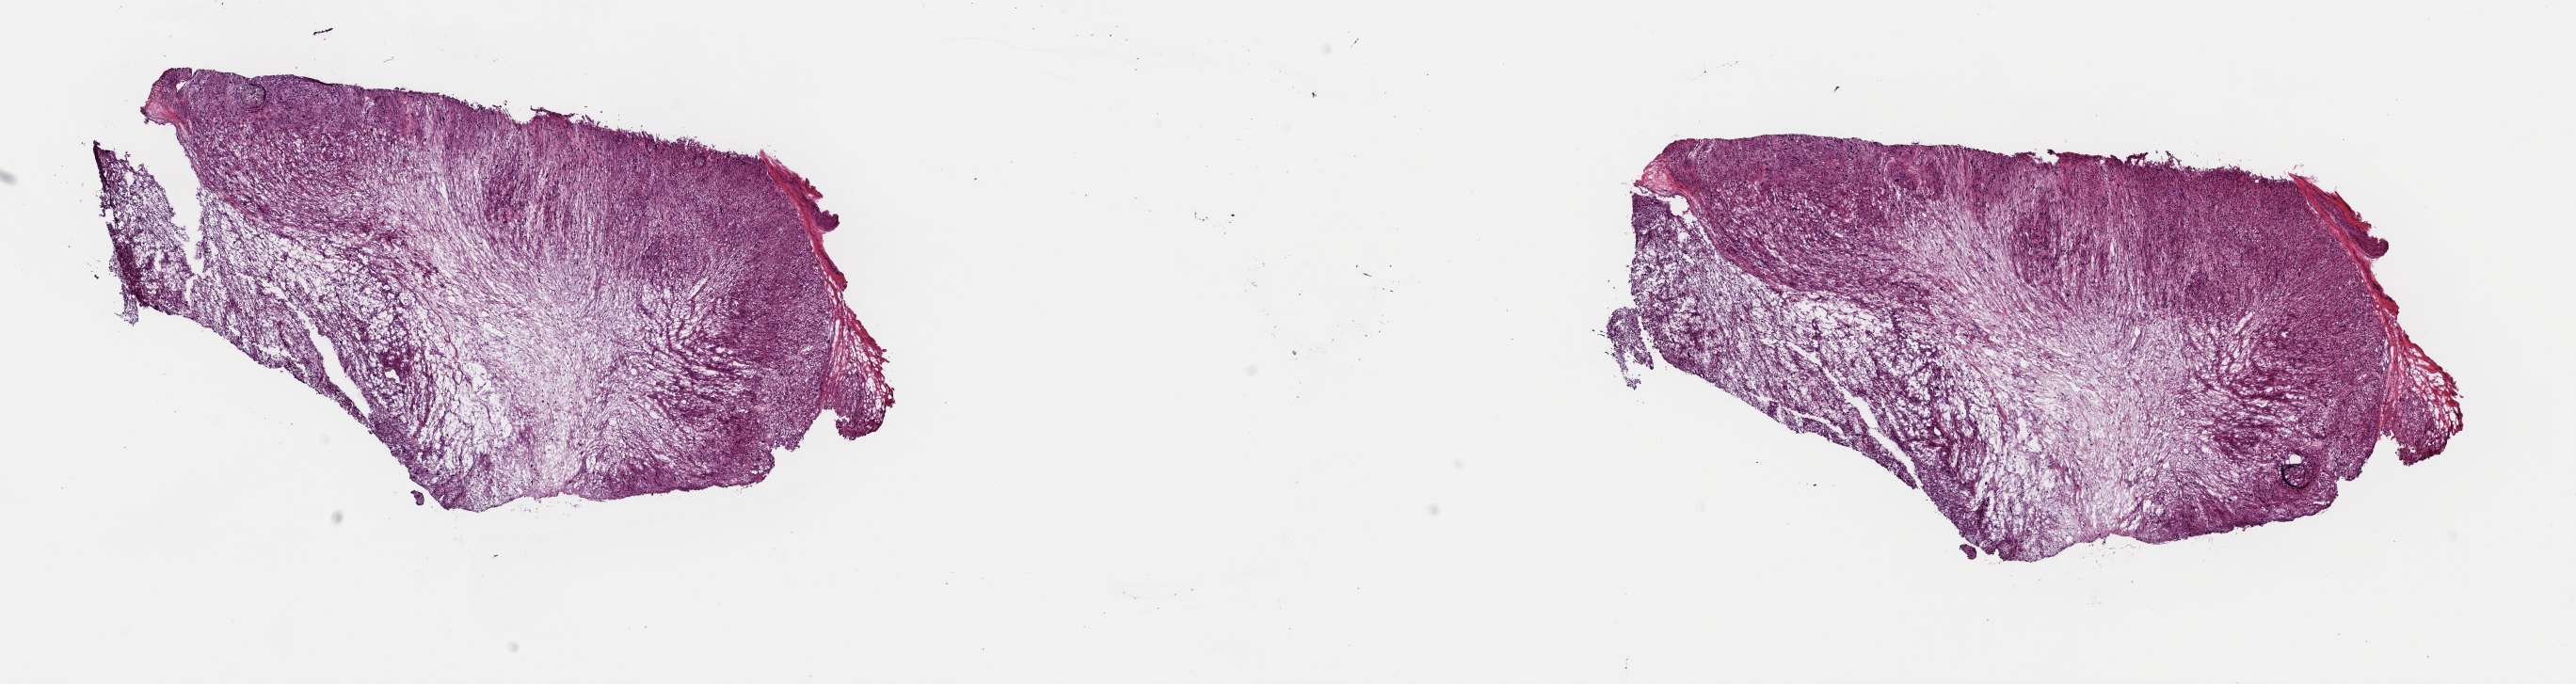
H&E whole-slide image — shown as a low-resolution overview of the whole scanned area (about 21.6 x 5.7 mm, acquisition: 40x scan). Frozen section from the top of the tissue portion. Sample: primary tumour, retroperitoneum and peritoneum. Patient: male, age at initial diagnosis 84 years. Pathologist review of this section (percent, as recorded): tumour cells 60%, tumour nuclei 80%, normal cells 0%, stromal cells 40%, necrosis 0%. Infiltration values recorded for this section: lymphocyte infiltration 0%, monocyte infiltration 0%, neutrophil infiltration 0%.
- diagnosis: Leiomyosarcoma, NOS (retroperitoneum)